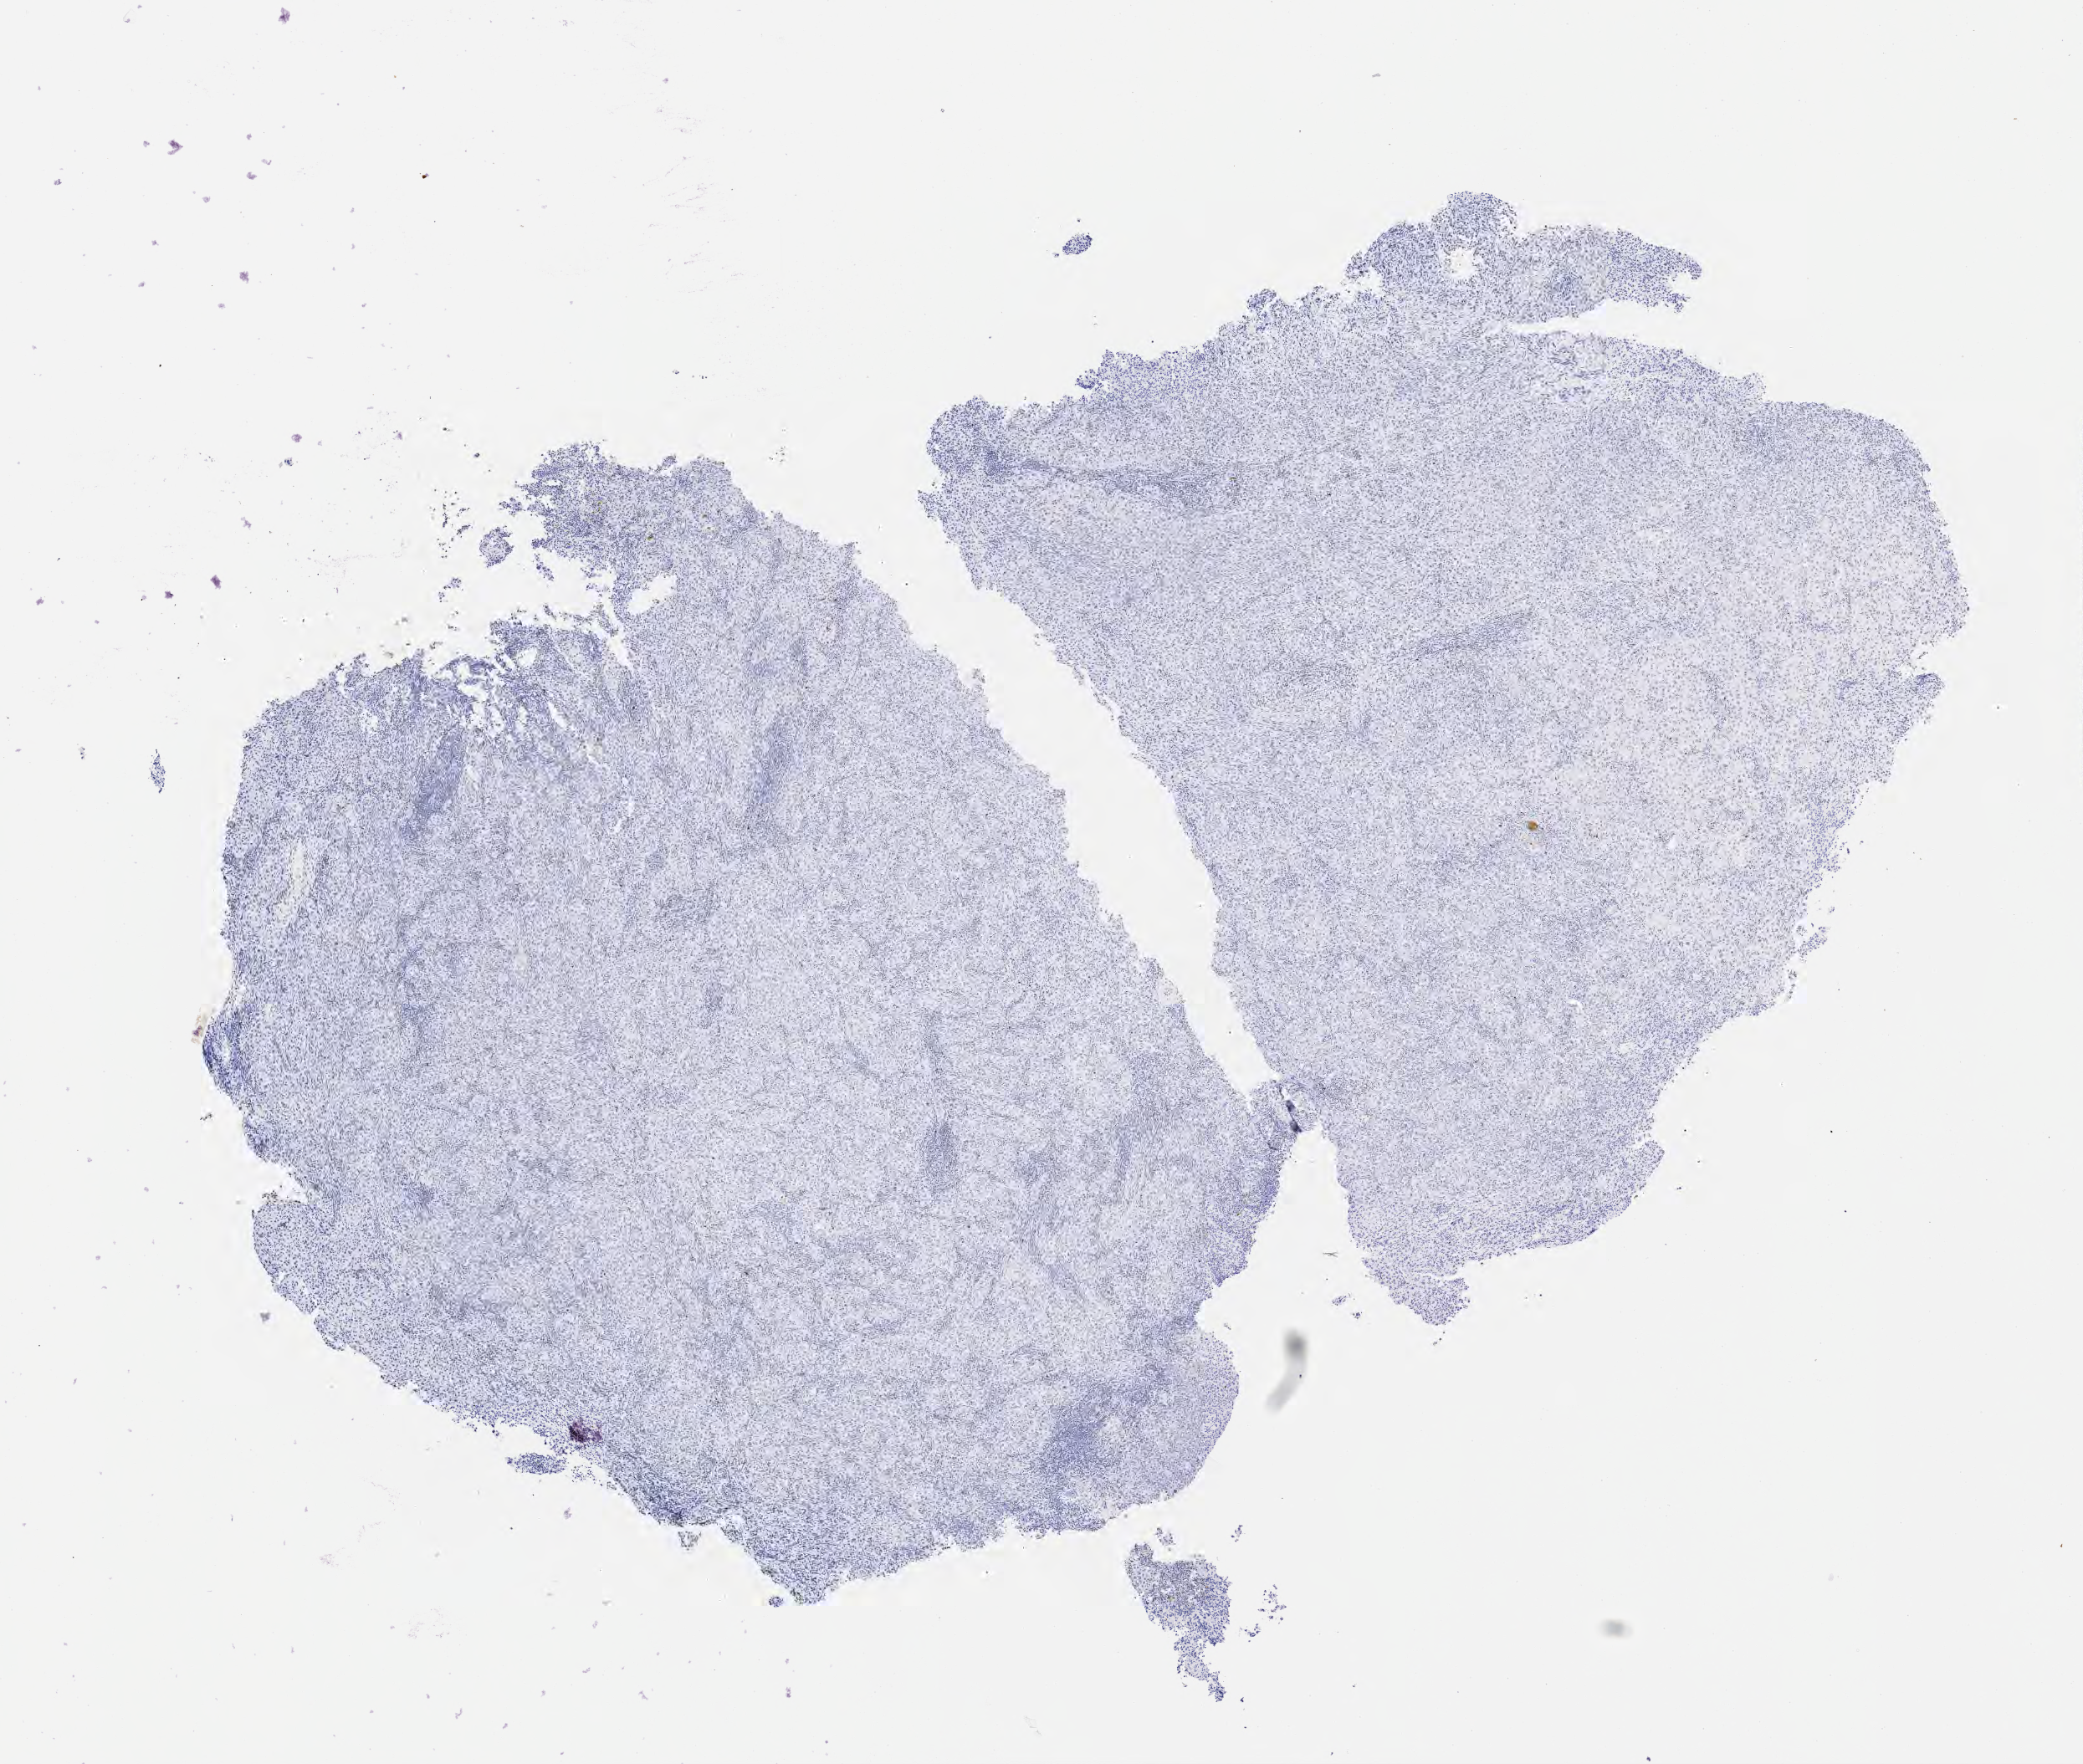
Whole-slide image, immunohistochemical stain for p16 (p16INK4a) — low-resolution overview of the scanned area, about 10.1 x 8.5 mm. Specimen: tumor tissue. Anatomic site: cervix. Patient female; aged 42.
- diagnosis: Neoplasm, uncertain whether benign or malignant